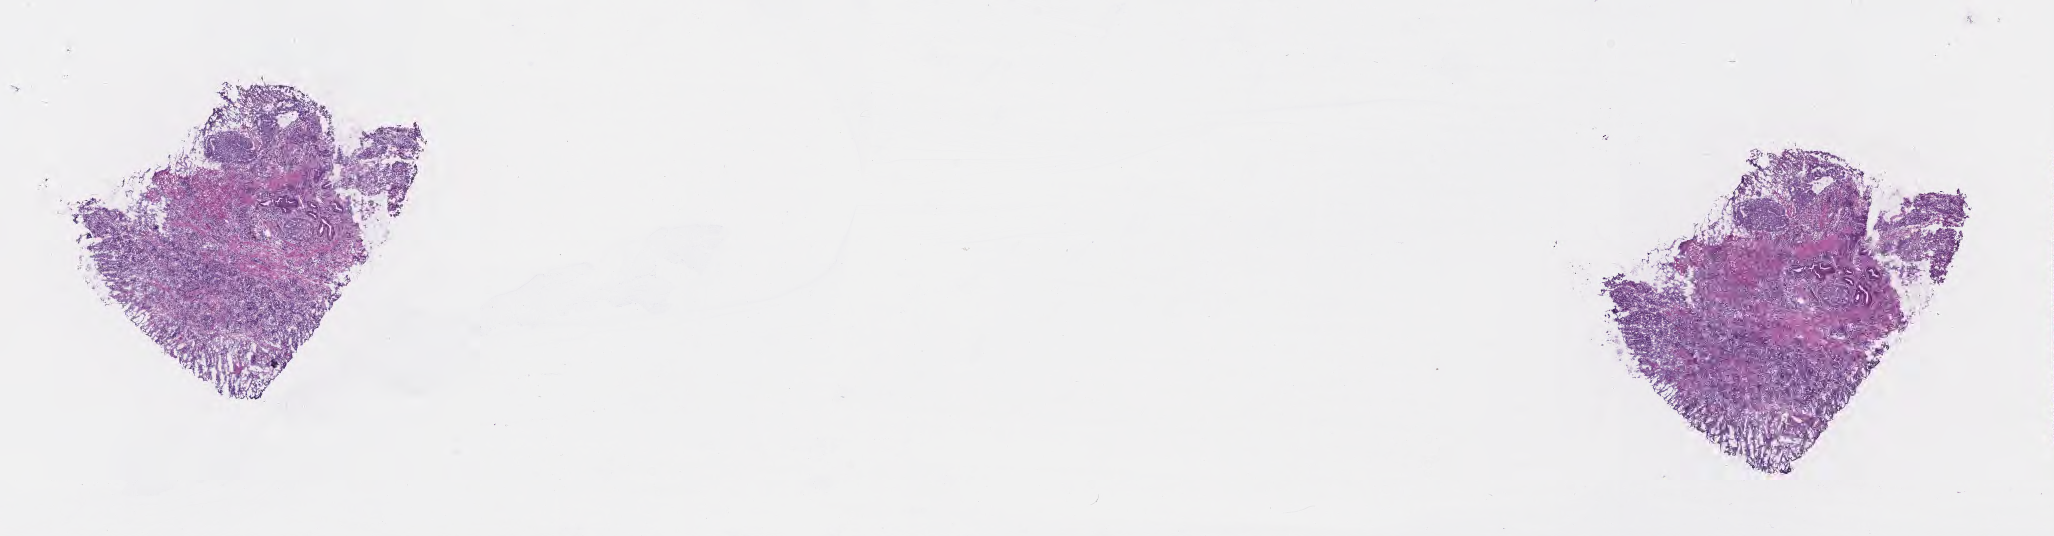
H&E whole-slide image — low-resolution overview of the scanned area, about 16.6 x 4.3 mm; frozen section (tissue freezing medium); specimen: primary tumor; site: ampulla of vater. Male patient; age at initial diagnosis 70 years.
Diagnosis: Adenocarcinoma, NOS.